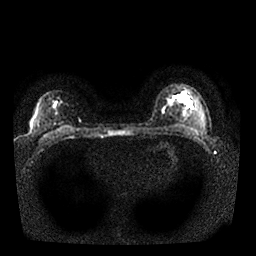
Breast MRI, one axial slice; slice 18 of 25 in the series (ordered by position); diffusion-weighted series; image 2 of 4 stored at this slice position (different b-values; order by instance number); 1.5 T; 4 mm slice thickness; 256 × 256 image matrix, field of view 340 × 340 mm. Female patient.
Annotated regions visible in this slice (manually delineated by an expert):
- tumour on diffusion-weighted imaging: box from (x=178, y=93) to (x=188, y=103) px